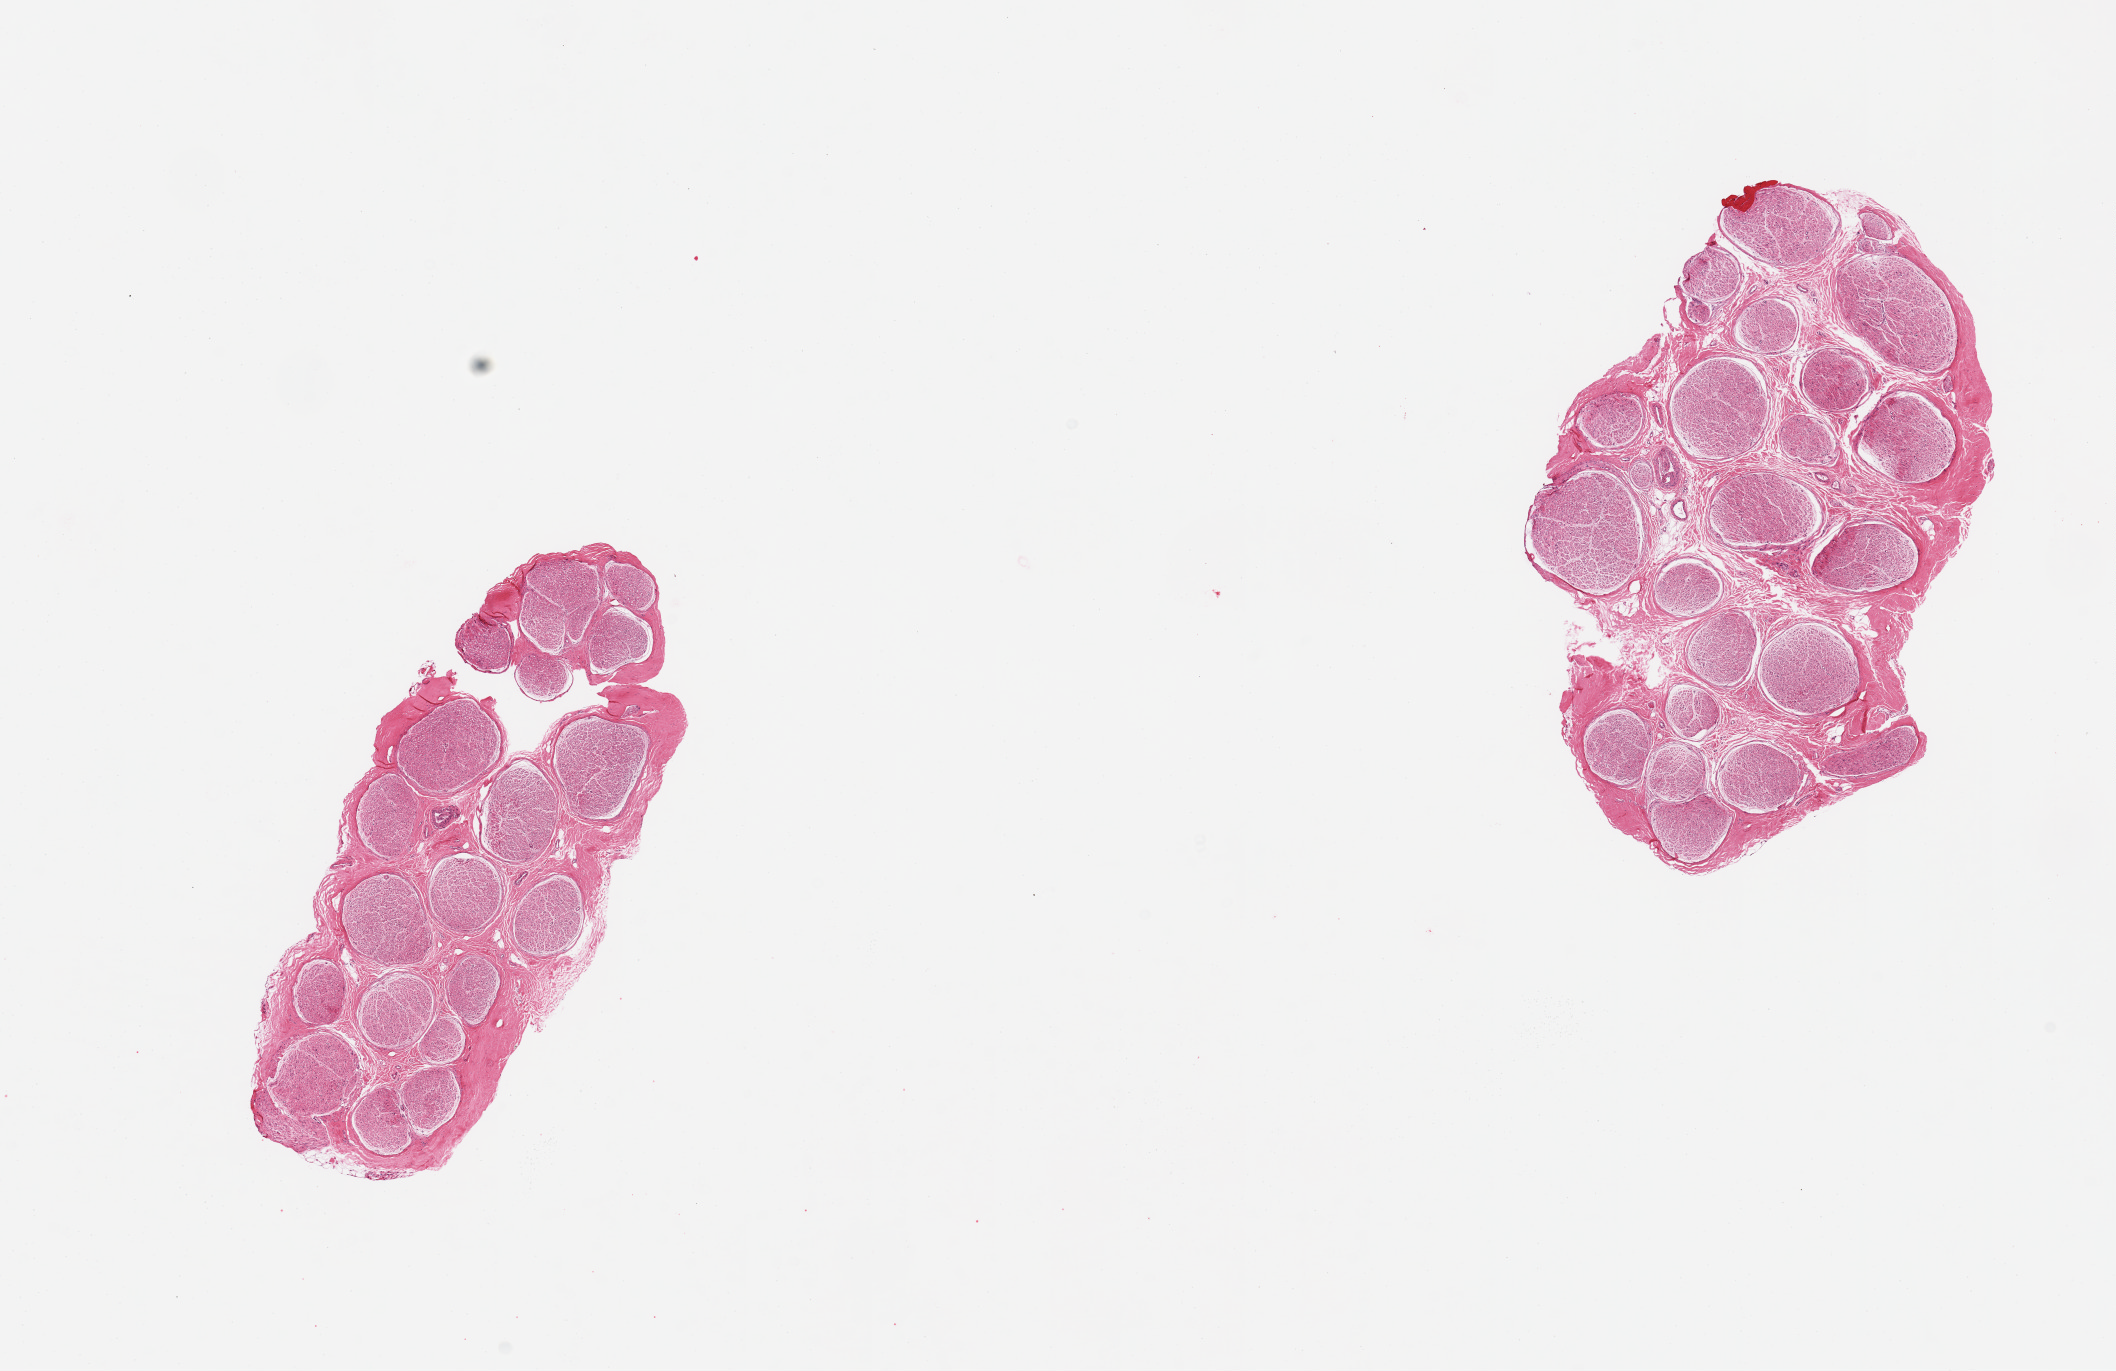
Whole-slide image, haematoxylin and eosin stain, whole scanned area (about 16.7 x 10.8 mm, acquisition: 20x scan) shown as a low-resolution overview. PAXgene-fixed, paraffin-embedded tissue. Target tissue: tibial nerve. Tissue donor sample. Donor: male.
Review note (as recorded): 2 pieces, no adherent fat.